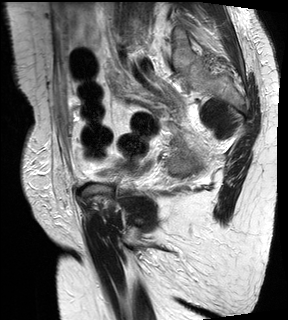
Pelvic MRI for cervical cancer, one sagittal slice; position 8 of 28 along the scan axis; T2-weighted; 1.5 T; TE 89 ms, TR 2740 ms; 288 × 320 image matrix, field of view 234 × 260 mm. Female patient, age 59 years.
Structures marked on this image (manually delineated by an expert):
- uterus and cervix: box from (x=167, y=132) to (x=204, y=177) px